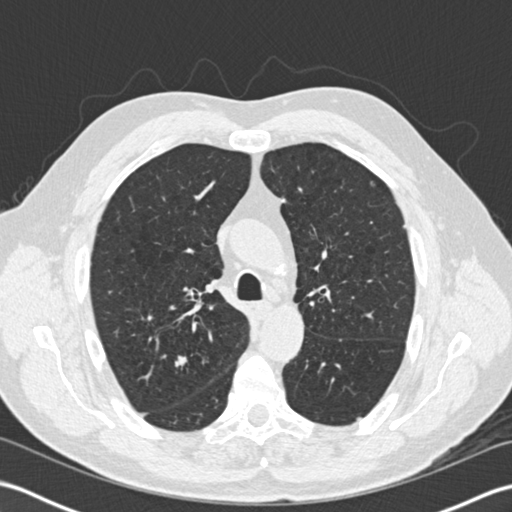
Low-dose screening chest CT, axial slice. Second annual screen. Lung window (W 1500 / L -600 HU). 2 mm slice thickness. 120 kVp. 512 × 512 image matrix. Male participant, aged 65 years at enrolment.
Expert reader's lesion annotation, box from (x=158, y=349) to (x=202, y=385) px. The screening reader recorded 6 non-calcified nodules or masses ≥4 mm on this exam; which of them this box marks is not recorded. Official screen result: positive, other. Lung cancer was diagnosed 421 days after this screen: adenocarcinoma, NOS, right upper lobe, moderately differentiated (G2), stage IA (AJCC 6th edition), 16 mm at pathology.